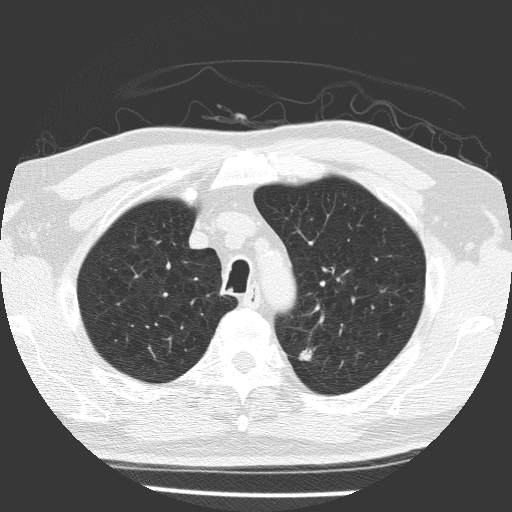
Chest CT (low-dose screening protocol), one axial image, baseline annual screen, lung window (W 1500 / L -600 HU), 2 mm slice thickness. Male participant, aged 64 years at enrolment.
• Expert-annotated lung lesion, bounding box [x1, y1, x2, y2] px = [287, 339, 325, 376].
• Reader record for this screening exam (exam-level; its link to the box is not recorded): non-calcified nodule or mass ≥4 mm, left upper lobe, 9 × 7 mm, spiculated (stellate) margins, soft tissue attenuation.
• Official screen result: positive, change unspecified: nodule(s) >= 4 mm or enlarging nodule(s), mass(es), or other non-specific abnormalities suspicious for lung cancer.